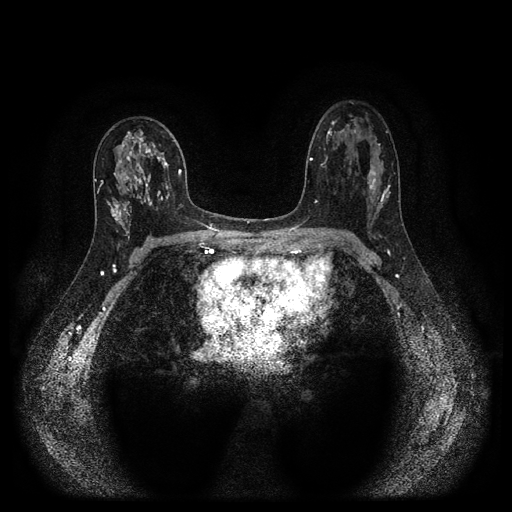
Breast MRI (dynamic contrast-enhanced, multi-phase), one axial slice. Position 61 of 116 along the scan axis. Dynamic contrast-enhanced series, time point 2 of 5 at this slice position (early post-contrast). 1.5 T. TE 2.7 ms, TR 5.4 ms. 2 mm slice thickness. 512 × 512 image matrix, field of view 330 × 330 mm. Patient: female, 47 years.
Annotated regions visible in this slice (semi-automatically segmented with operator editing):
- breast lesion (labelled 'tumour' in the annotation; benign lesions carry a separate 'benign' label): box from (x=114, y=128) to (x=175, y=211) px